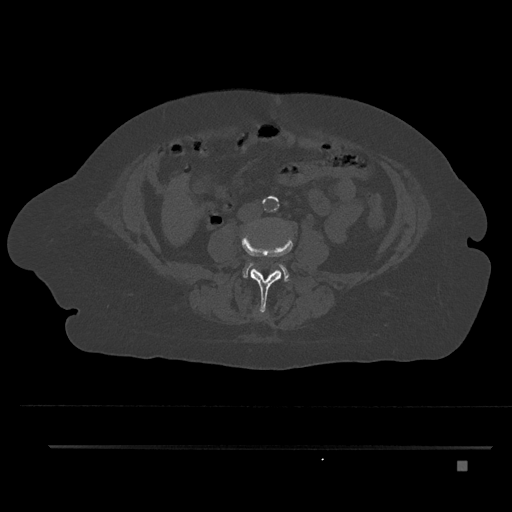
CT including the spine, one axial slice. Position 114 of 797 along the scan axis. 120 kVp. Bone window (W 1800 / L 400 HU). 512 × 512 image matrix, field of view 437 × 437 mm. Female patient, age 76 years. From the clinical record (not read from this slice): primary cancer: lung; vertebrae with lytic lesions (as recorded): T11, L3.
Outlined on this slice (semi-automatic segmentation, software-assisted and operator-edited):
- L2 vertebra: bounding box (x1, y1, x2, y2) in pixels: (255, 311, 263, 315)
- L3 vertebra: (241, 233, 293, 312)
- L4 vertebra: (243, 262, 289, 282)